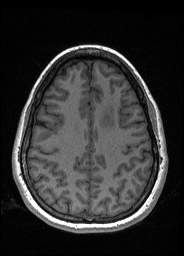
Pre-operative brain MRI before brain-tumour surgery, one axial slice; slice 65 of 176 in the series (ordered by position); T1-weighted post-contrast; 1 mm slice thickness; 184 × 256 image matrix, field of view 180 × 250 mm. From the clinical record (not read from this slice): histopathology: Oligodendroglioma; WHO grade: 2; IDH mutation: yes; tumour location: Left Frontal.
Outlined on this slice (manually delineated by an expert):
- tumour: bounding box (x1, y1, x2, y2) in pixels: (100, 102, 116, 128)